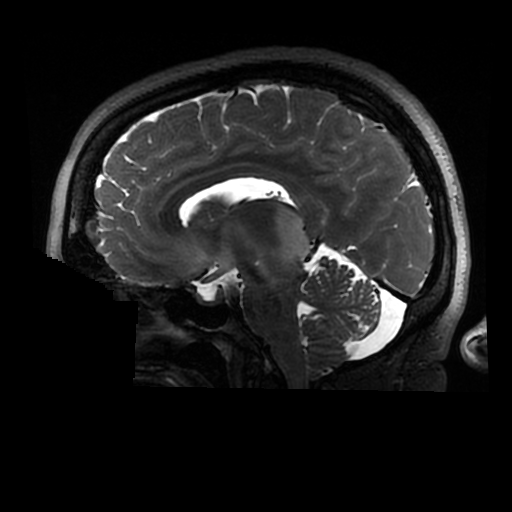
Brain MRI from a brain-tumour surgery series, one sagittal slice. Slice 162 of 320 in the series (ordered by position). 0.6 mm slice thickness. 512 × 512 image matrix, field of view 240 × 240 mm. Case-level facts recorded for this patient, not image findings: histopathology: Astrocytoma; WHO grade: 2; IDH mutation: yes.
Structures marked on this image (outlined manually by an expert reader):
- tumour: bounding box [x1, y1, x2, y2] px = [273, 205, 311, 266]